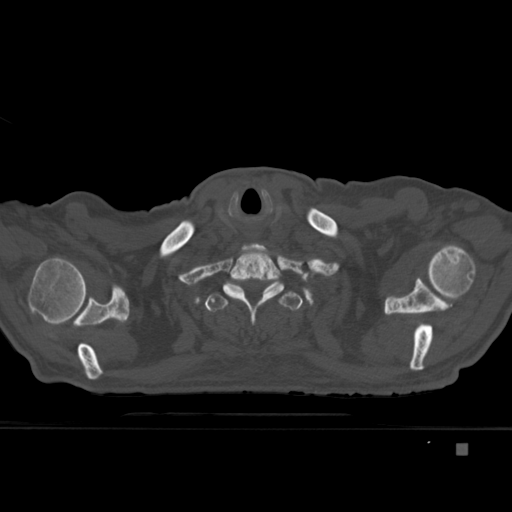
CT including the spine, one axial slice. Slice 356 of 451 in the series (ordered by position). Bone window (W 1800 / L 400 HU). 512 × 512 image matrix, field of view 378 × 378 mm. Patient: male, 75 years. From the clinical record (not read from this slice): primary cancer: prostate.
Outlined on this slice (semi-automatic segmentation, software-assisted and operator-edited):
- T1 vertebra: bounding box (x1, y1, x2, y2) in pixels: (223, 243, 285, 325)
- T2 vertebra: (205, 285, 303, 312)